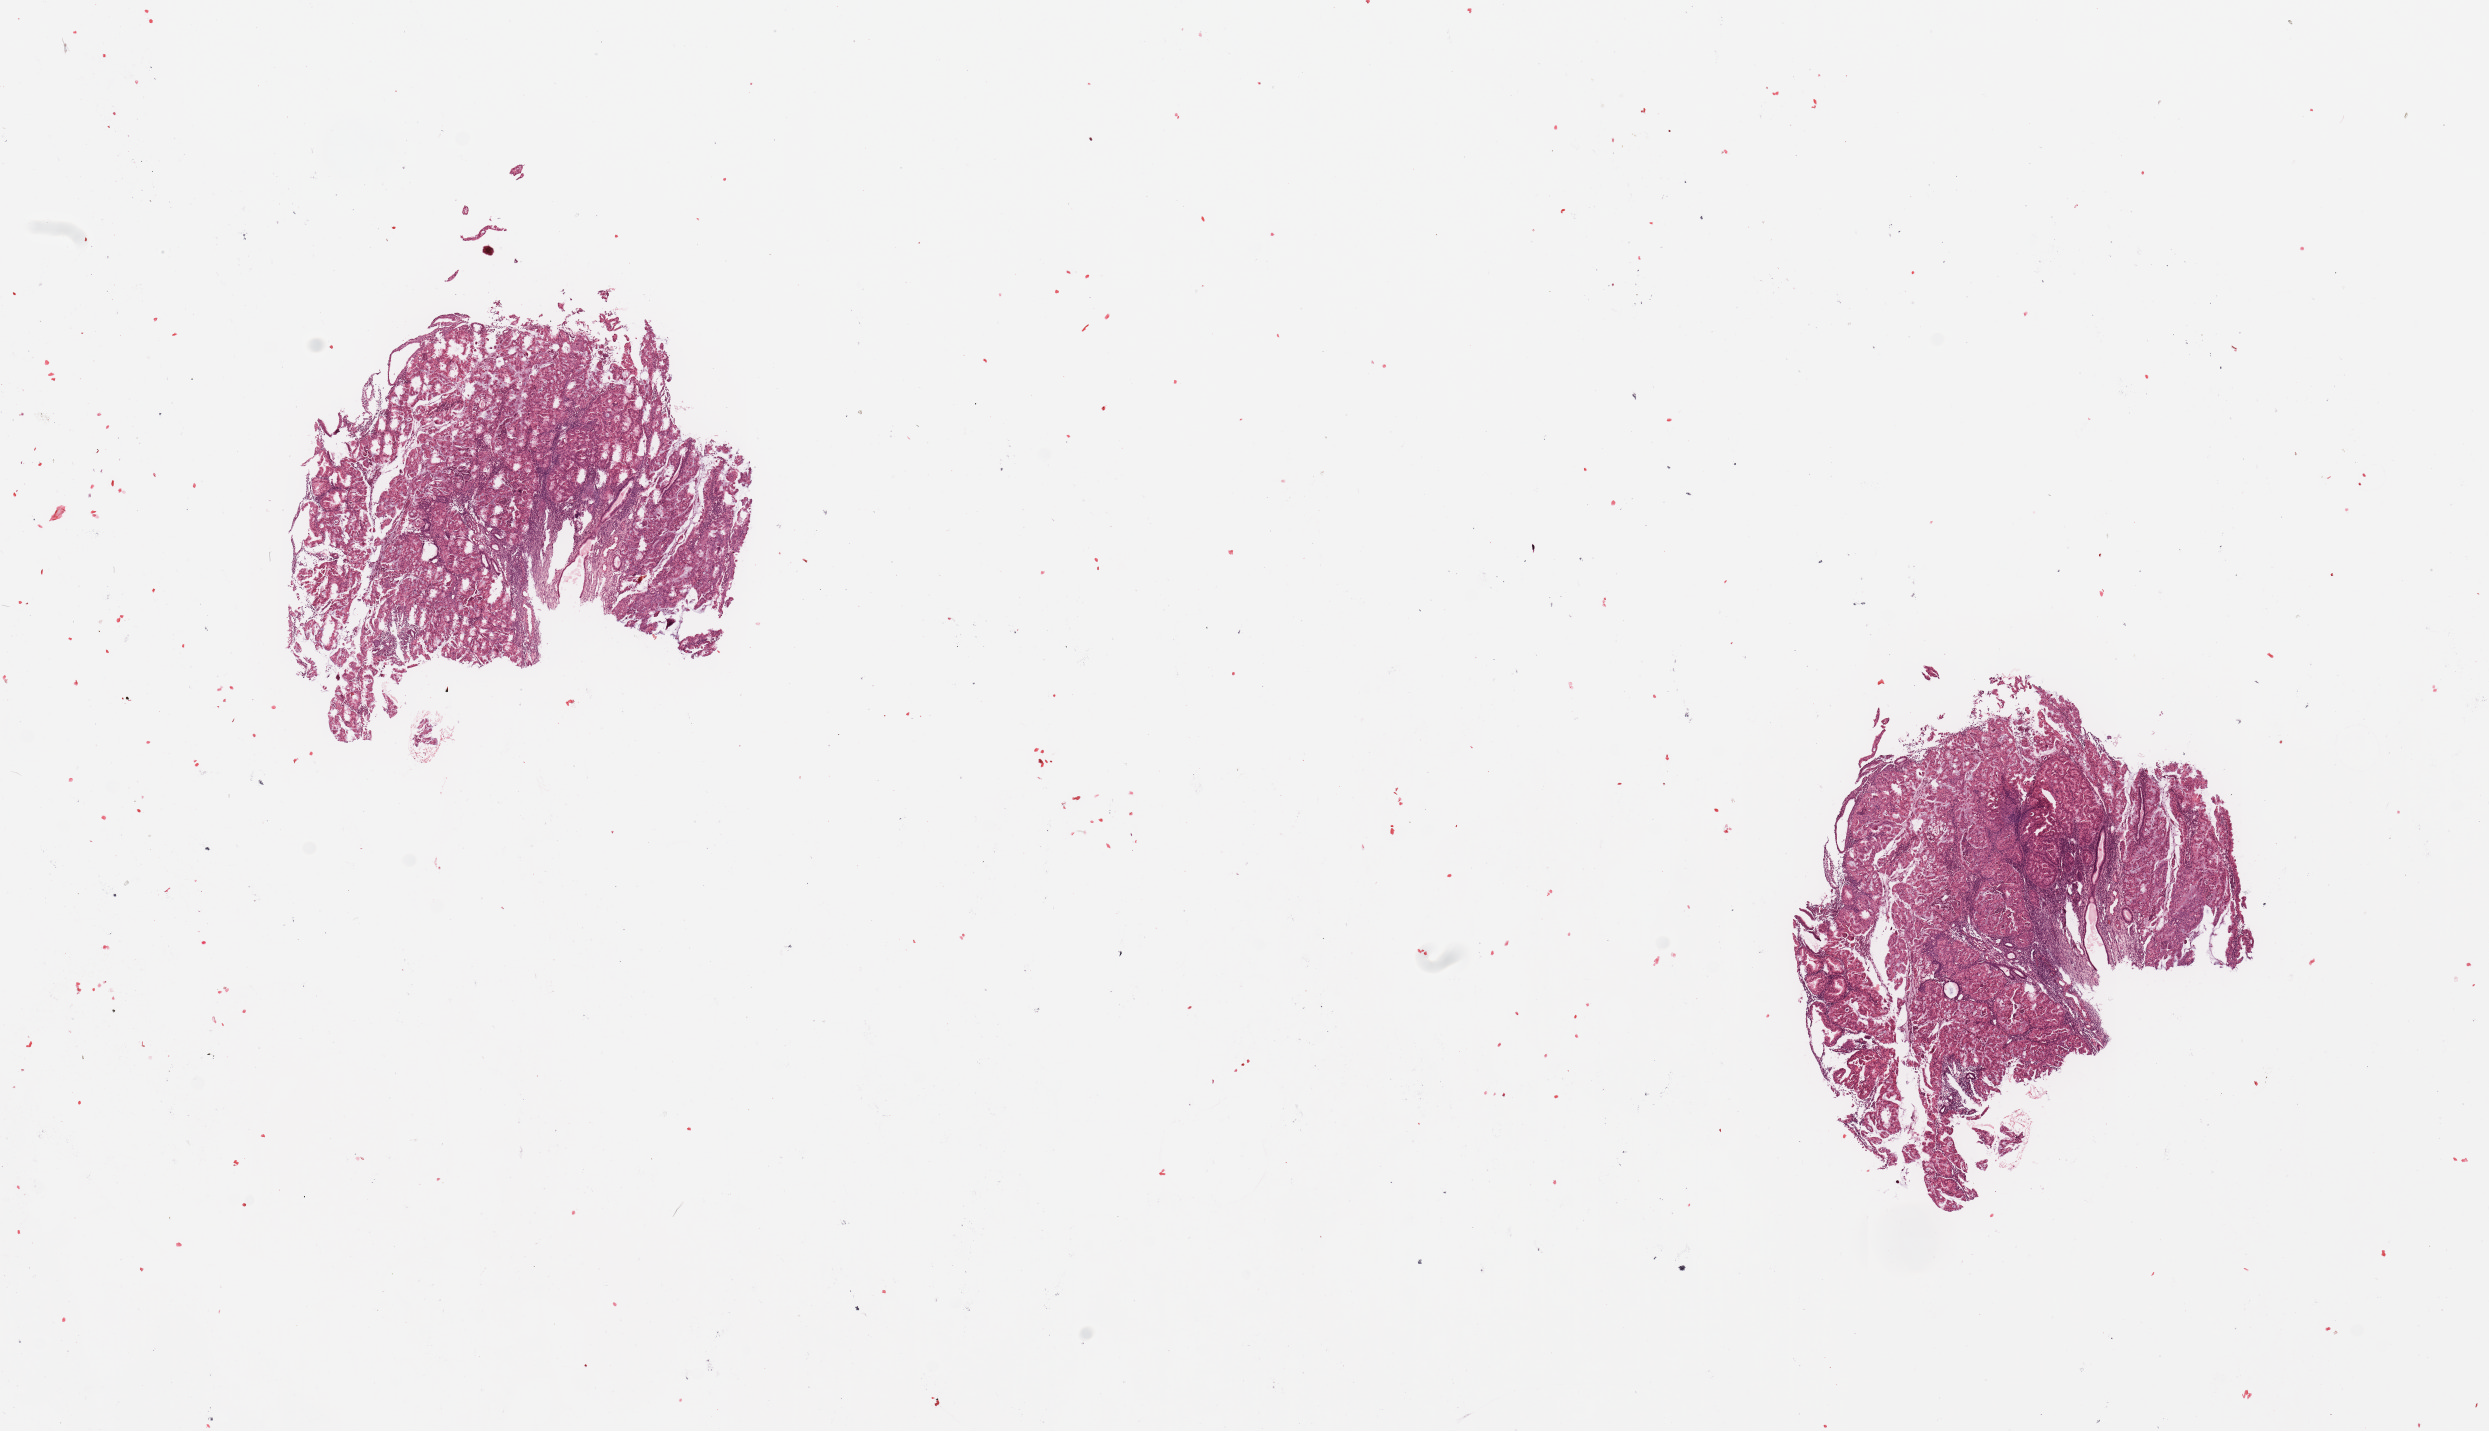
Whole-slide histology image, Hematoxylin and eosin (H&E) stained — low-resolution overview of the scanned area, about 19.7 x 11.3 mm; uterus, tumour tissue. 58-year-old female patient. Histologic grade: G2 (moderately differentiated).
* histologic diagnosis: Endometrioid adenocarcinoma, NOS
* primary tumour site (as recorded): anterior endometrium
* AJCC pathologic stage: I